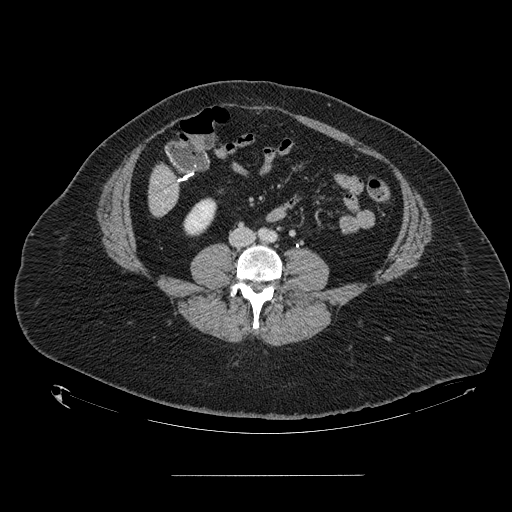
Contrast-enhanced abdominal CT, one axial slice; position 16 of 164 along the scan axis; intravenous contrast given; soft-tissue window (W 400 / L 40 HU); 2.5 mm slice thickness; 512 × 512 image matrix, field of view 495 × 495 mm. Female patient, age 52 years. From the clinical record (not read from this slice): diagnosis: colorectal cancer liver metastases, imaged before liver resection; multiple liver metastases: yes; largest metastasis: 3.5 cm; disease in both lobes: no.
Outlined on this slice (outlined manually by an expert reader):
- liver: box from (x=149, y=166) to (x=178, y=215) px